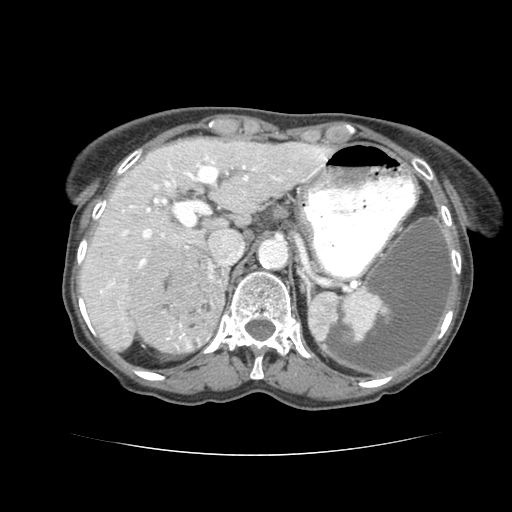
Contrast-enhanced abdominal CT (liver protocol), one axial slice. Slice 51 of 77 in the series (ordered by position). 120 kVp. Soft-tissue window (W 400 / L 40 HU). 512 × 512 image matrix, field of view 340 × 340 mm. Case-level facts recorded for this patient, not image findings: diagnosis: hepatocellular carcinoma (patient treated with transarterial chemoembolisation; whether this scan precedes or follows treatment is not stated here); TNM stage (as recorded): Stage-I; Child-Pugh class: A; tumour differentiation: well differentiated; tumour size: 7.6 cm.
Annotated regions visible in this slice (semi-automatic segmentation, software-assisted and operator-edited):
- liver parenchyma outside the tumour (the mass and vessels are separate outlines, so this box may not span the whole liver): bounding box (x1, y1, x2, y2) in pixels: (78, 135, 312, 346)
- mass: (129, 243, 223, 351)
- liver vessels: (90, 157, 275, 332)